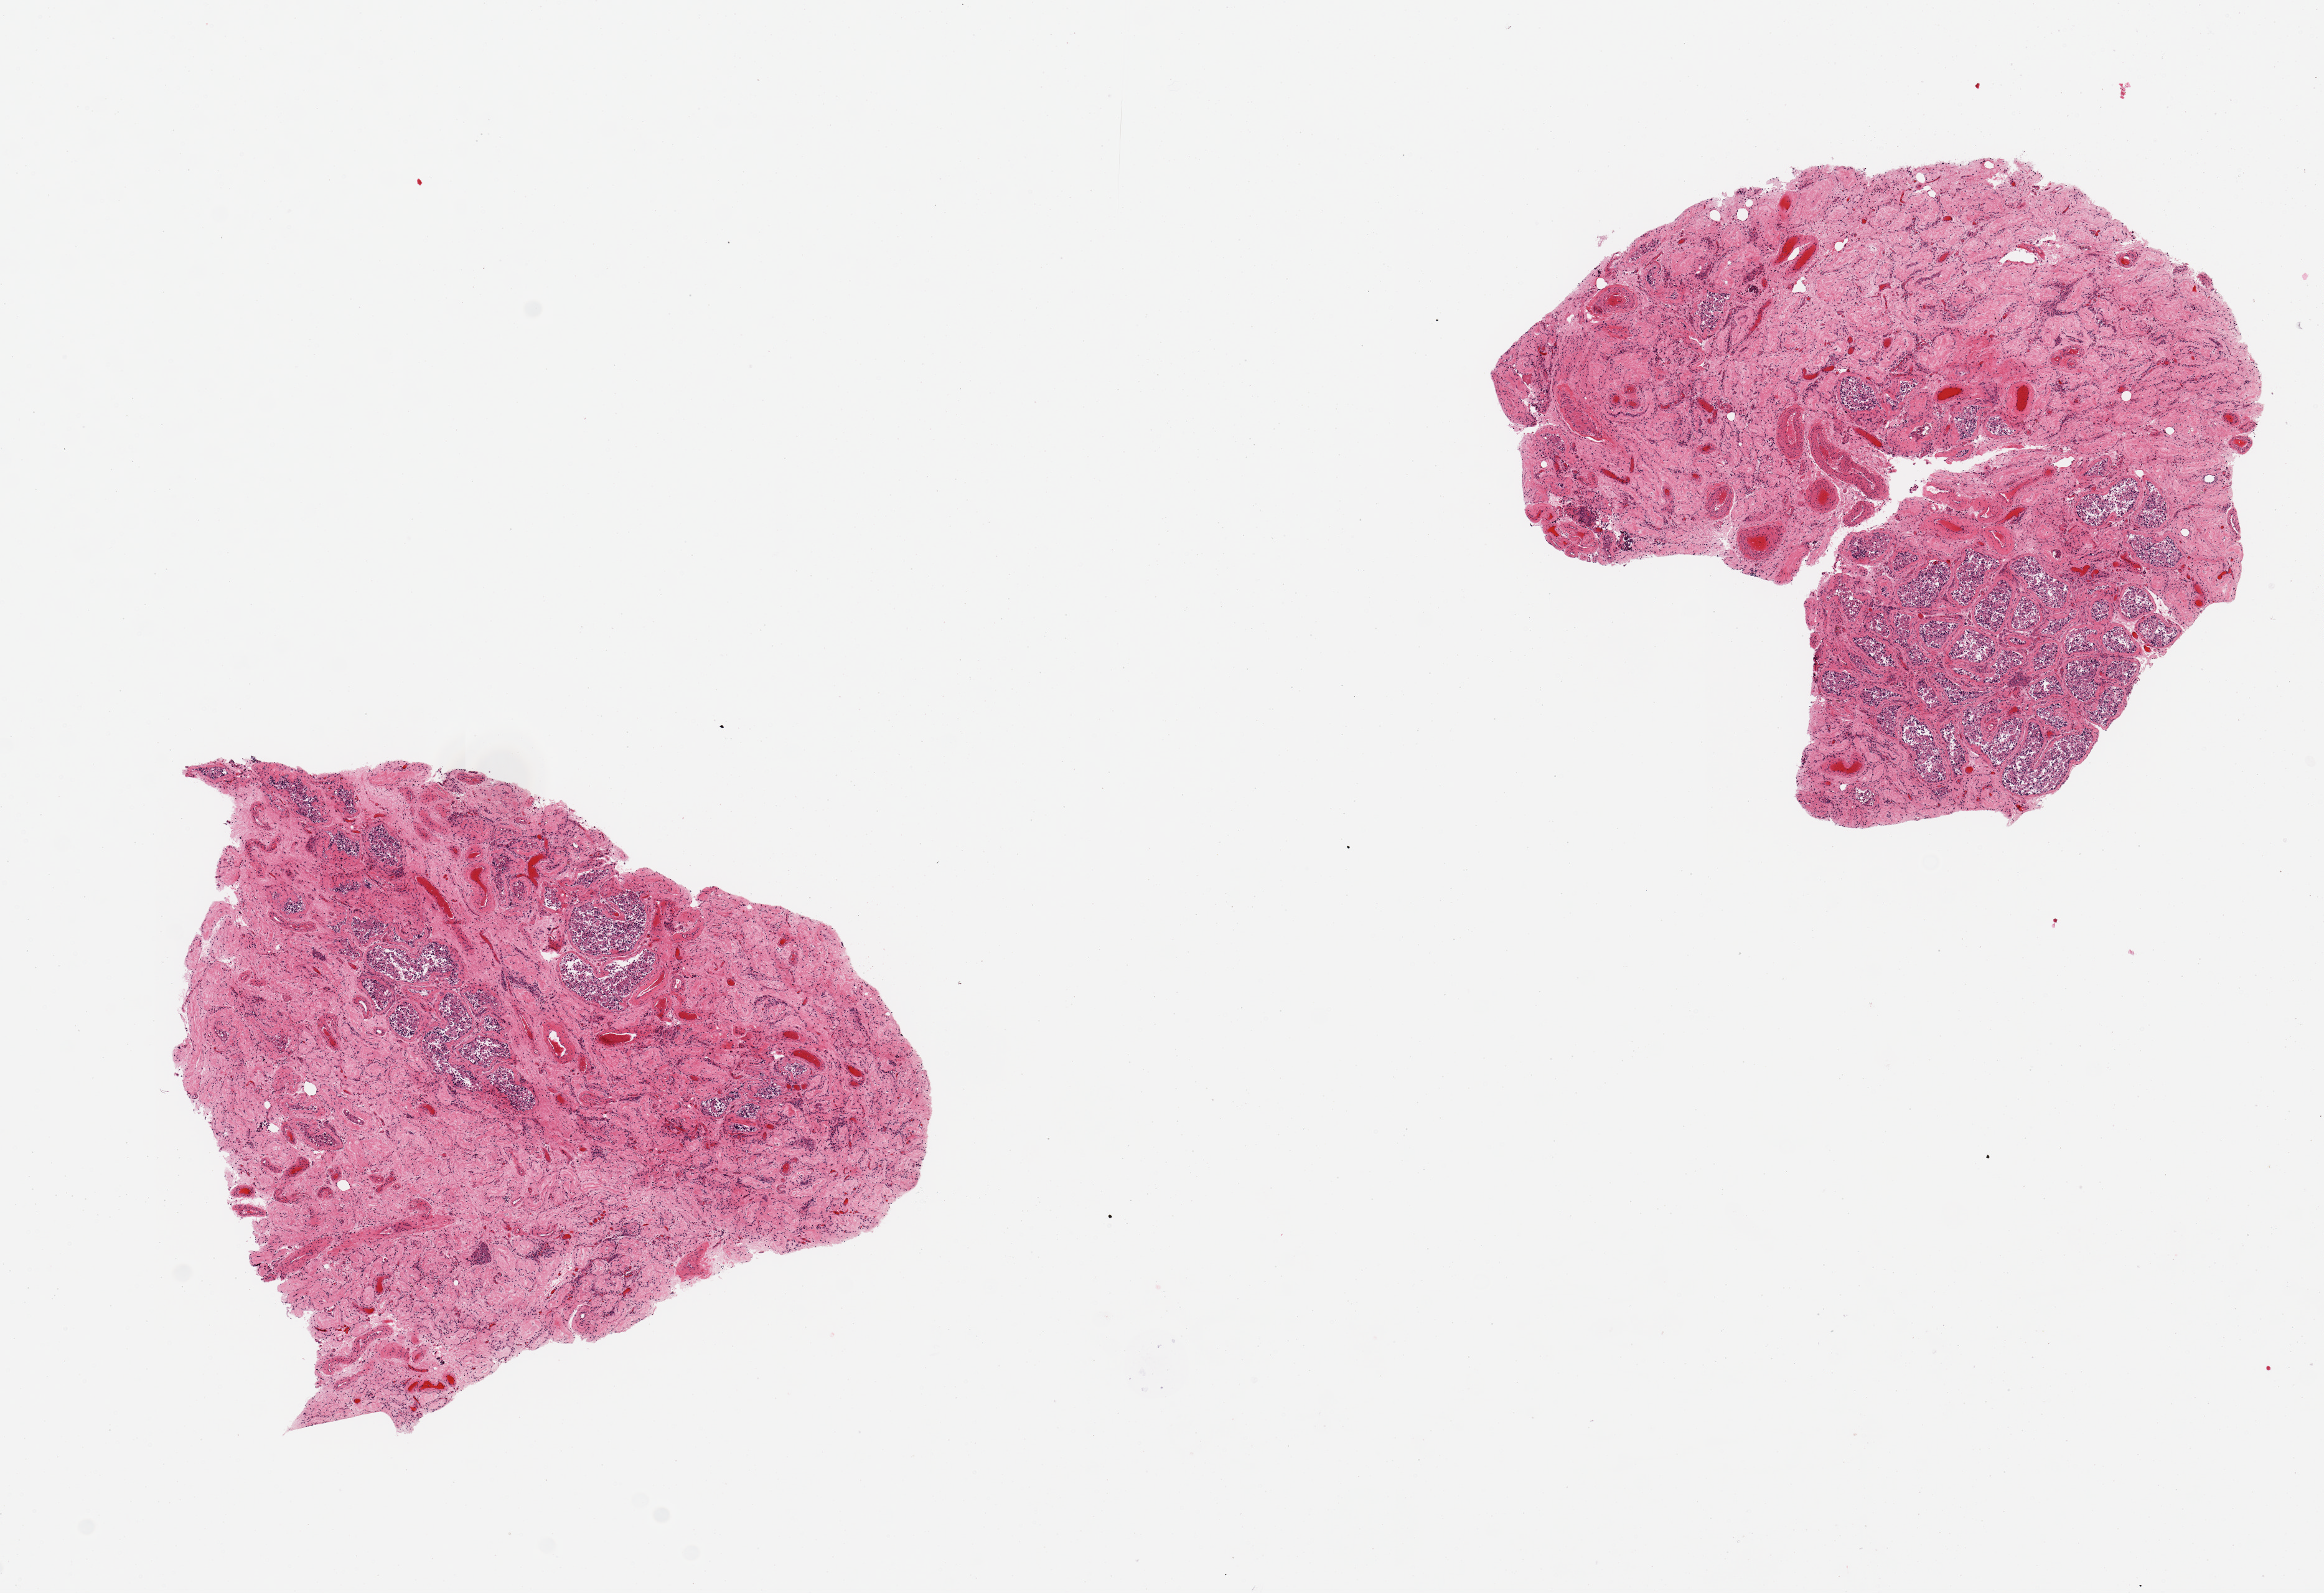
Digitized hematoxylin and eosin (H&E)-stained section — whole scanned area (about 14.8 x 10.1 mm, from a 20x scan) shown as a low-resolution overview. PAXgene-fixed paraffin-embedded (PFPE) section. Section of testis (target tissue). Tissue donor sample. Male donor.
* pathologist's review note for this sample: 2 pieces, marked tubular atrophy, diffuse, no Leydig hyperplasia noted. Rare foci of spermatogenesis but moderately-markedly autolyzed